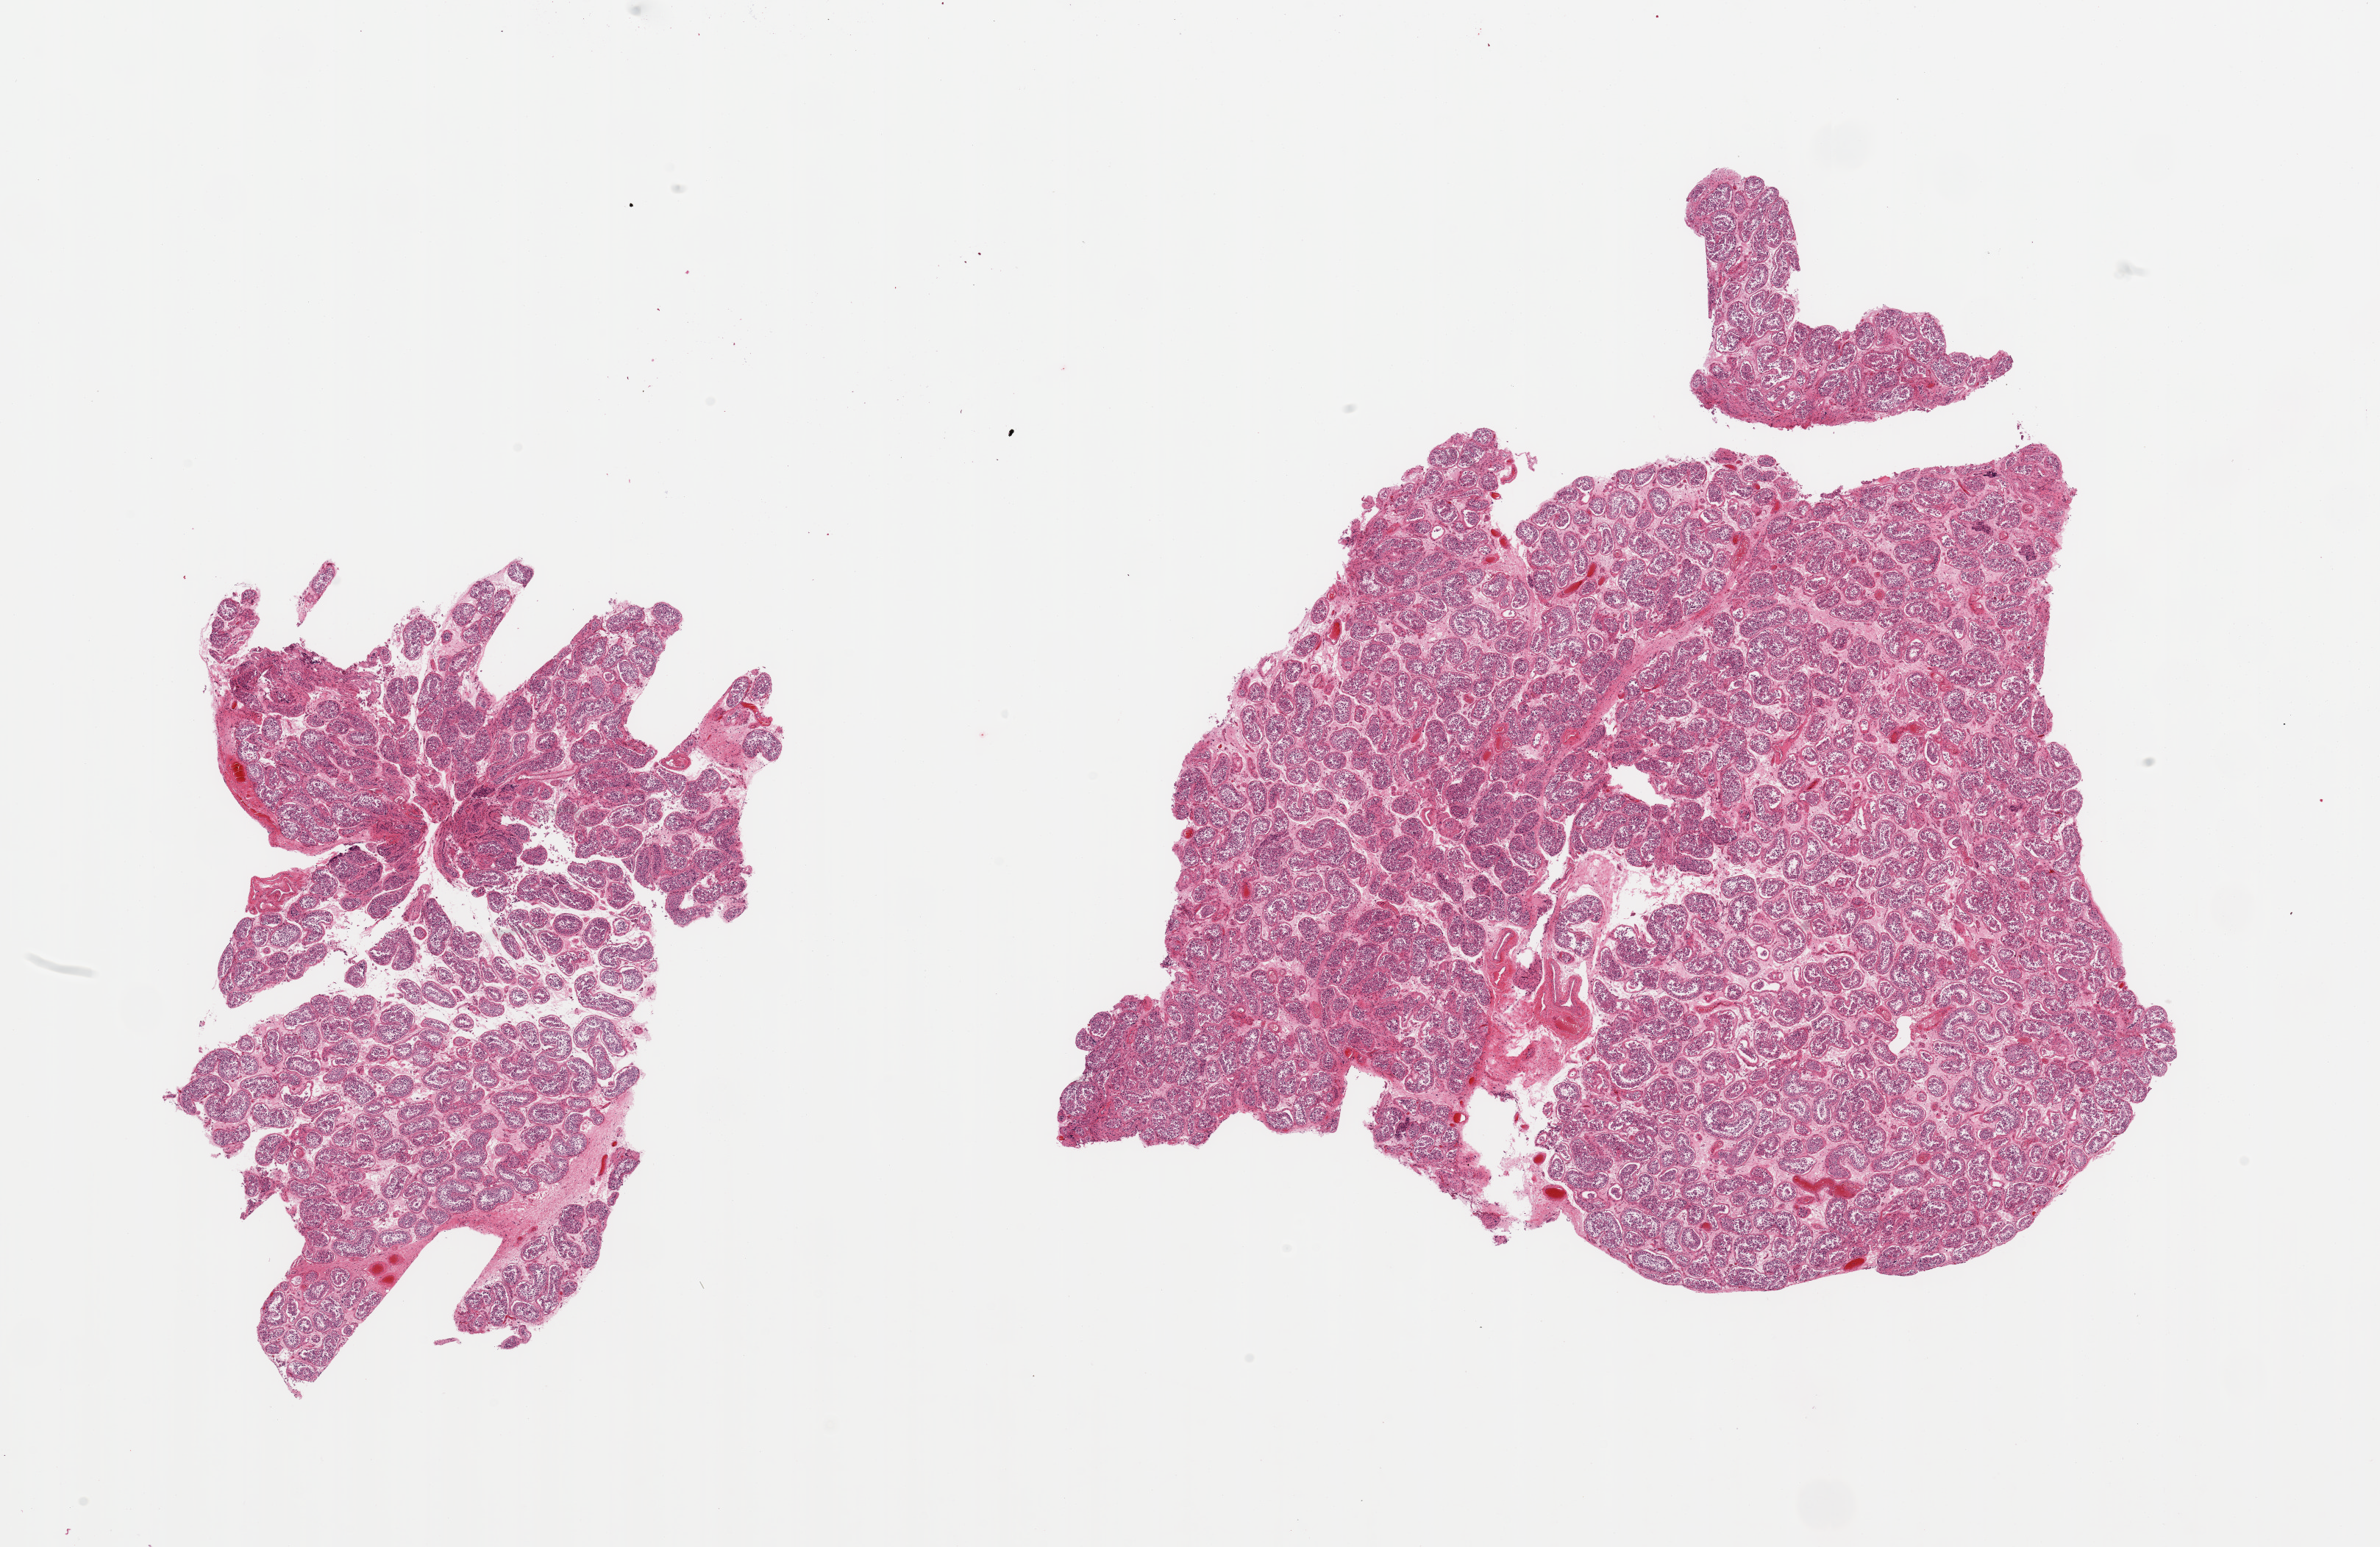
Digitized hematoxylin and eosin (H&E)-stained section — whole scanned area (about 25.6 x 16.6 mm, slide scanned at 20x) shown as a low-resolution overview, PAXgene-fixed paraffin-embedded (PFPE) section, sampled site (target tissue): testis, donor tissue sample.
Reviewer comment on this tissue sample: 2 pieces, spermatogenesis appears reduced.